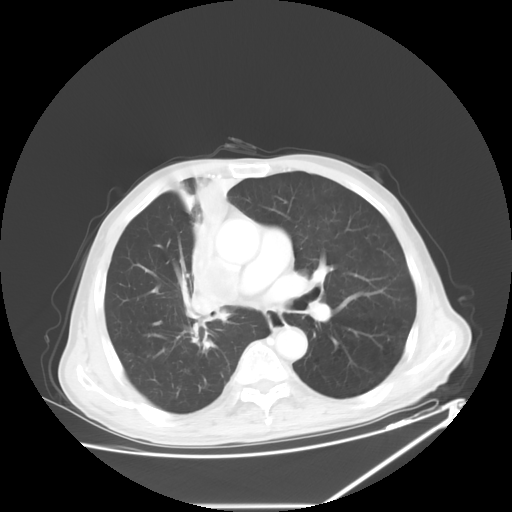
Chest CT, one axial slice; position 35 of 60 along the scan axis; 120 kVp; lung window (W 1500 / L -600 HU); 5 mm slice thickness; 512 × 512 image matrix, field of view 410 × 410 mm. Male patient, age 73 years. From the clinical record (not read from this slice): clinical TNM (as recorded): T2a N1 M0.
Annotated regions visible in this slice (rectangle marked by the reading radiologist):
- lung tumour (recorded histology: squamous cell carcinoma): bounding box [x1, y1, x2, y2] px = [182, 166, 245, 327]